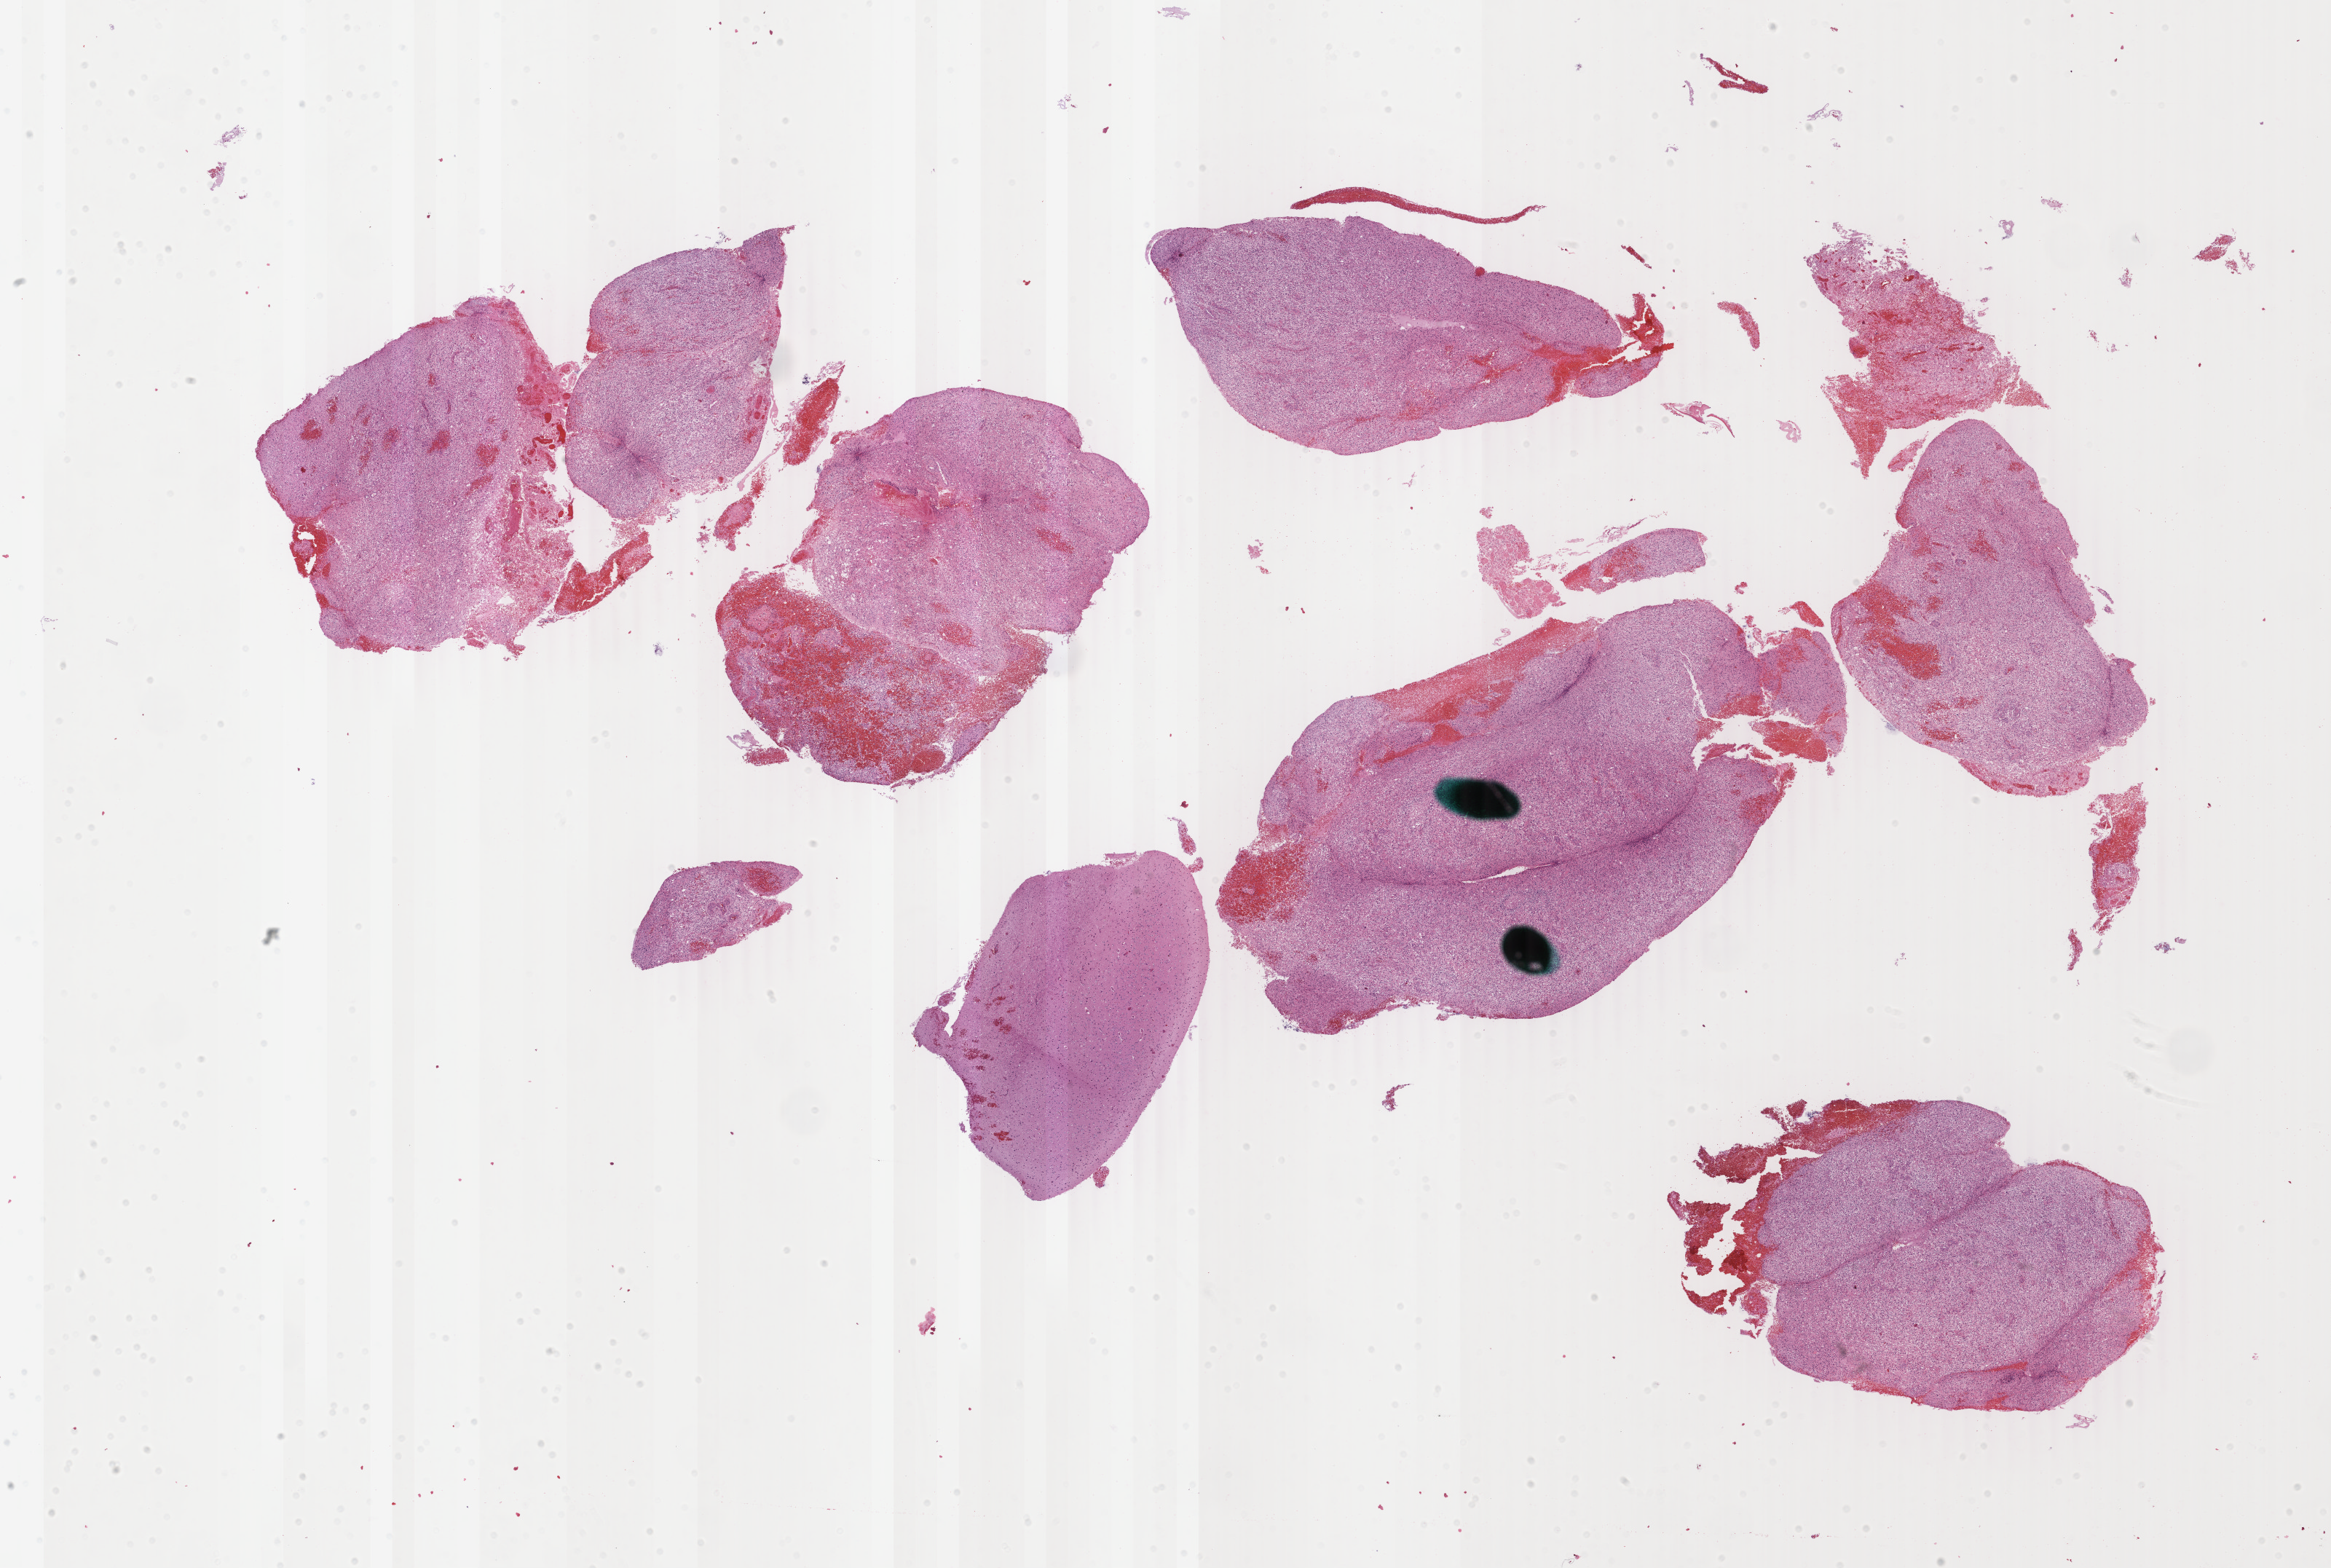
H&E-stained whole-slide image, low-resolution overview of the scanned area, about 25.5 x 17.1 mm, formalin-fixed paraffin-embedded (FFPE) diagnostic section, sample: primary tumour, brain. Female, age 72 years at initial diagnosis.
Diagnosis: Glioblastoma.